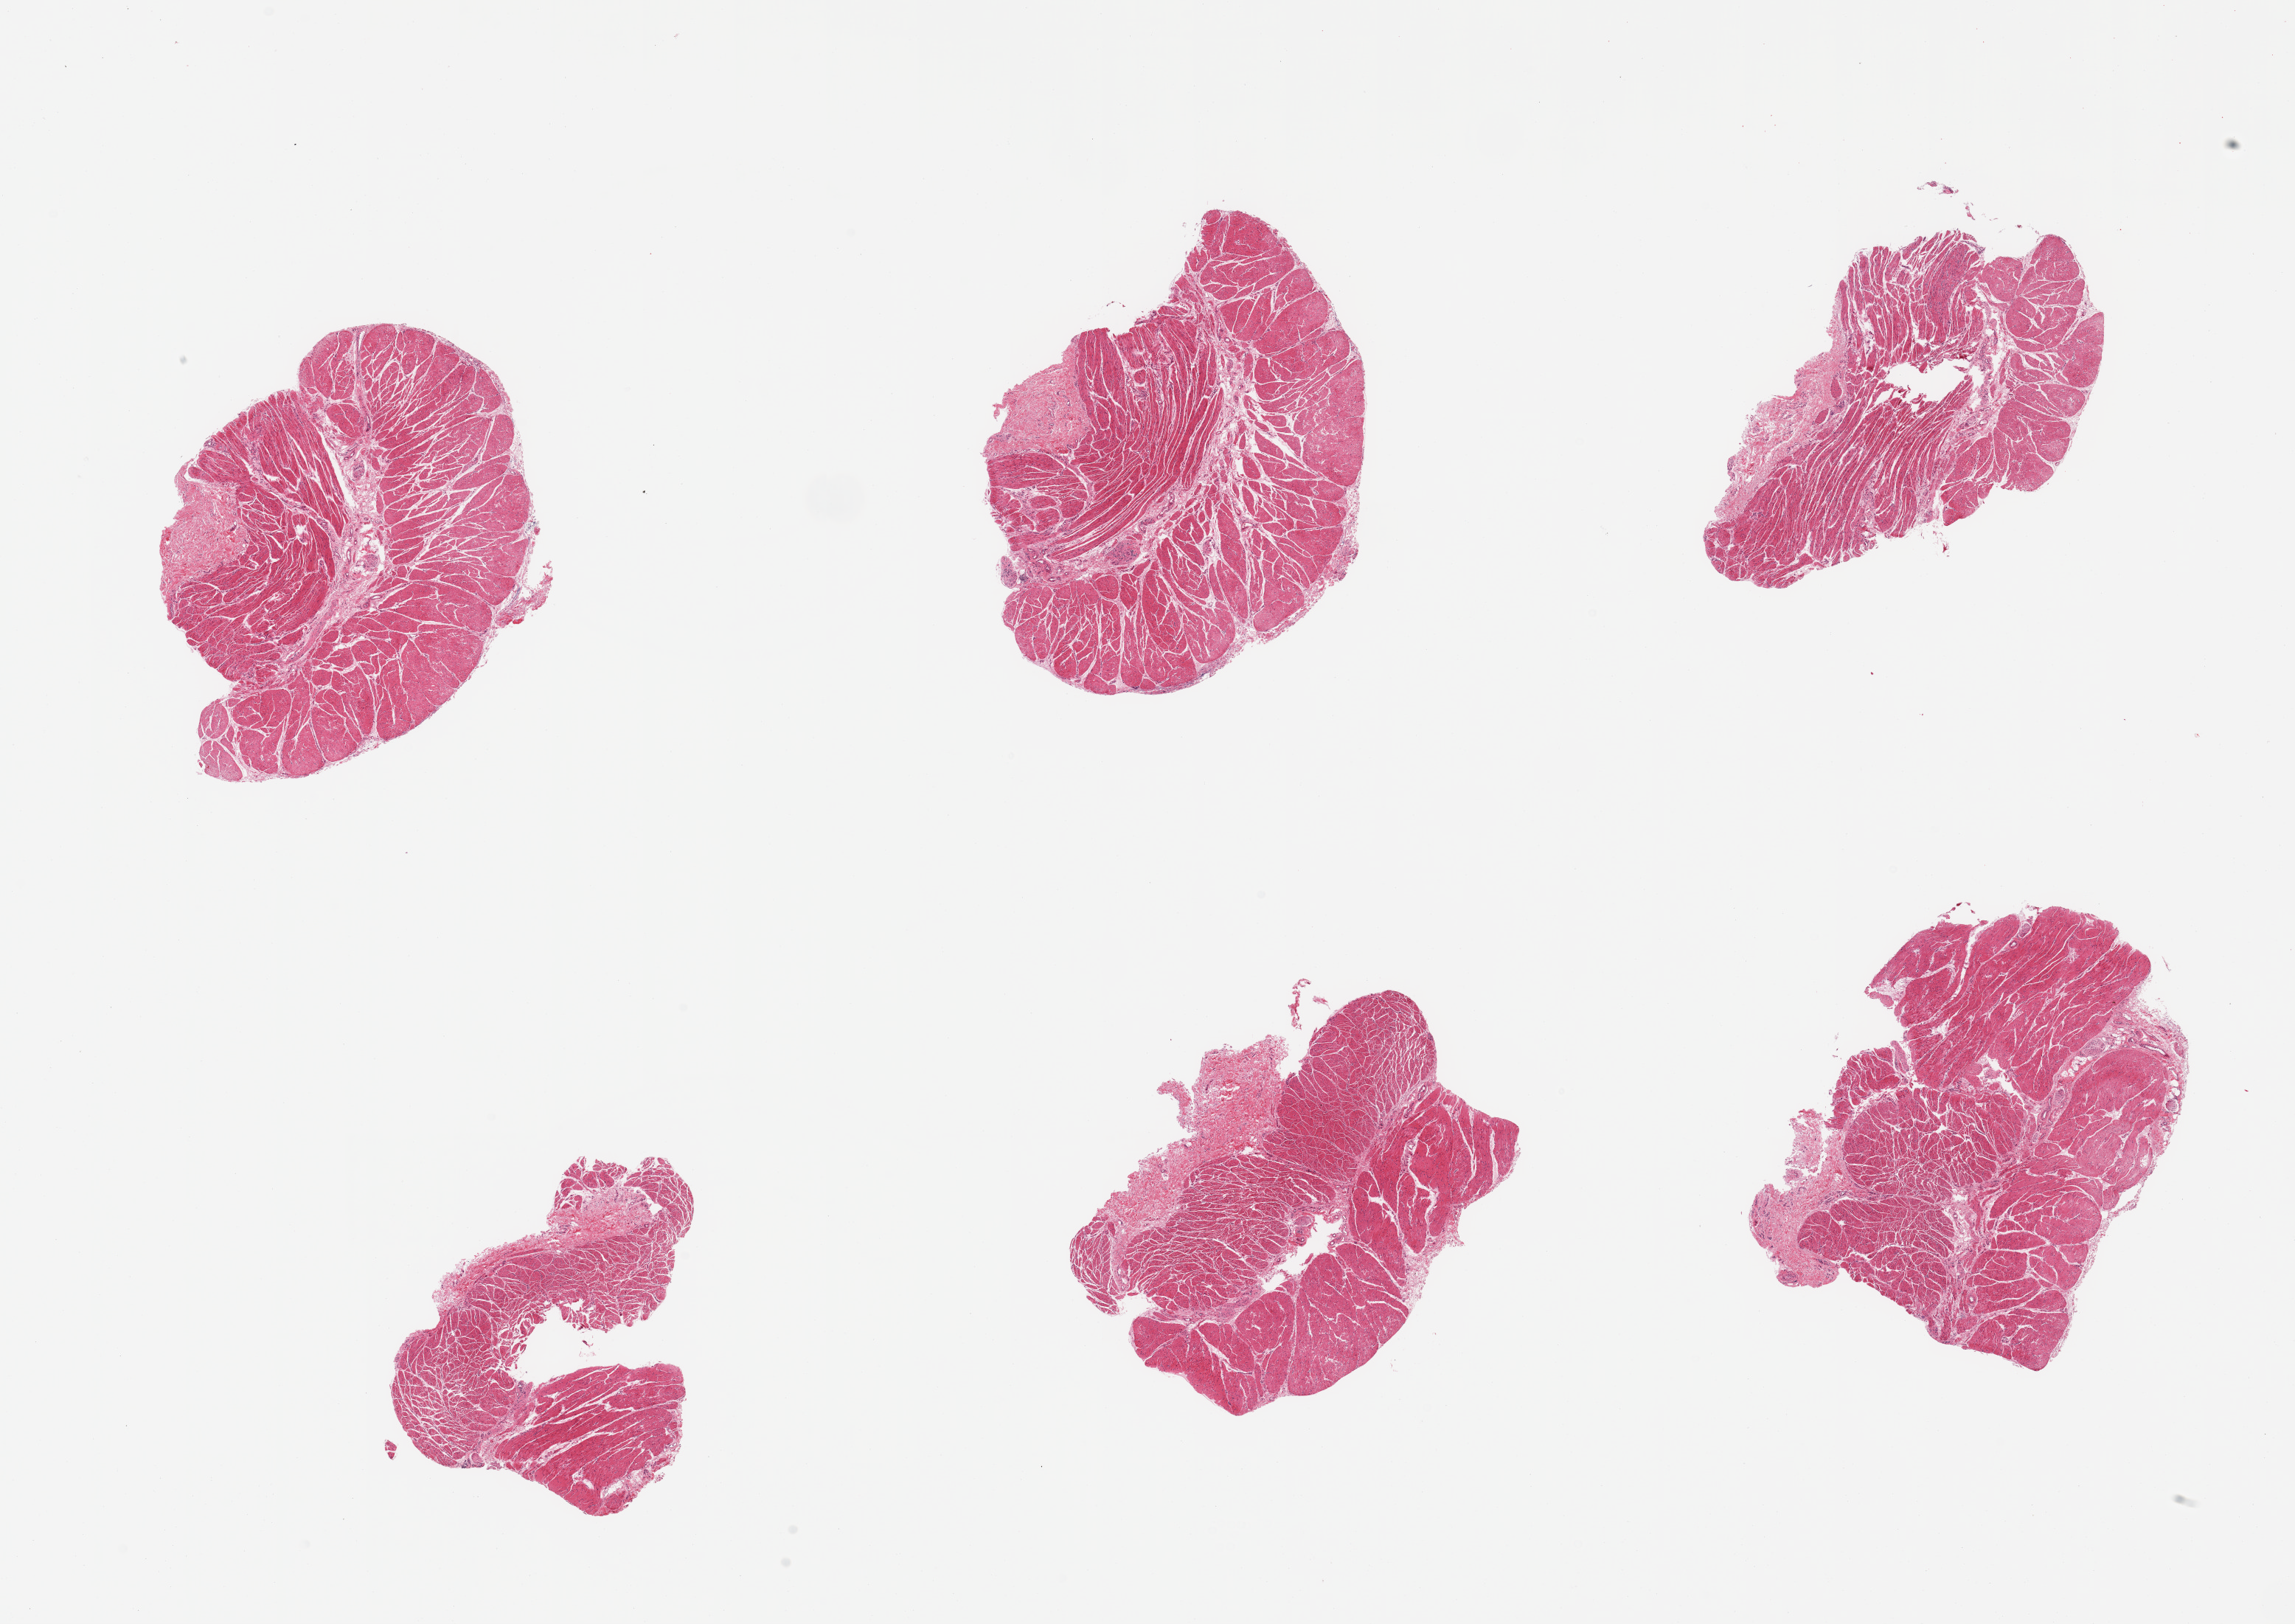
Hematoxylin and eosin (H&E) whole-slide image, brightfield, shown as a low-resolution overview of the whole scanned area (about 24.6 x 17.4 mm, acquisition: 20x scan), PAXgene-fixed paraffin-embedded (PFPE) section, section of esophageal muscle (target tissue), tissue donor sample.
Review note (as recorded): 6 pieces, confirmed target muscularis.